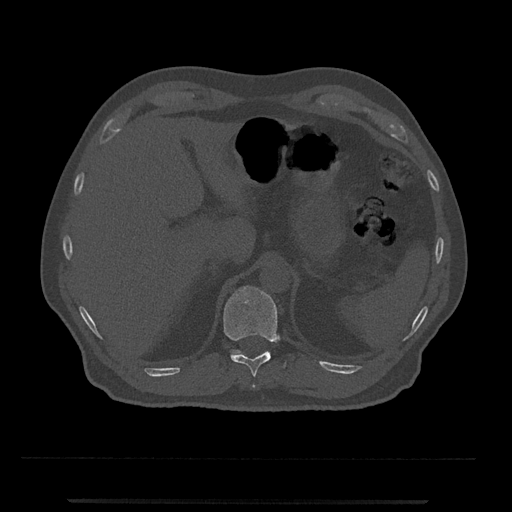
CT including the spine, one axial slice; slice 455 of 797 in the series (ordered by position); reconstruction kernel Br40s/3; 120 kVp; bone window (W 1800 / L 400 HU); 0.5 mm slice thickness; 512 × 512 image matrix, field of view 419 × 419 mm. Patient: male, 63 years. From the clinical record (not read from this slice): primary cancer: prostate.
Outlined on this slice (semi-automatically segmented with operator editing):
- T11 vertebra: bounding box <223,286,286,388> (left, top, right, bottom; pixels)
- T12 vertebra: <231,350,241,355>